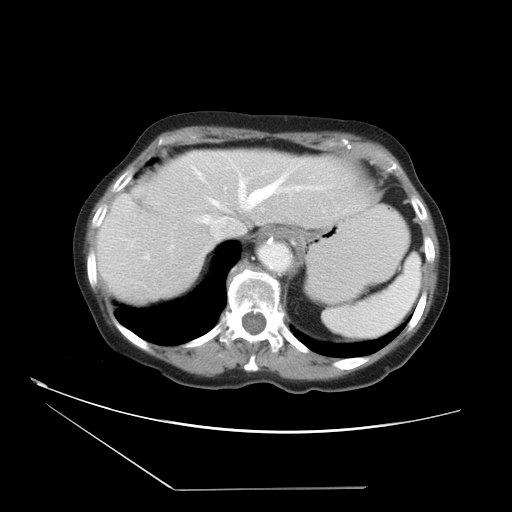
Contrast-enhanced abdominal CT, one axial slice; position 28 of 36 along the scan axis; 120 kVp; intravenous contrast given; soft-tissue window (W 400 / L 40 HU); 512 × 512 image matrix. Female patient, age 81 years. From the clinical record (not read from this slice): diagnosis: colorectal cancer liver metastases, imaged before liver resection; multiple liver metastases: no; largest metastasis: 1.6 cm.
Structures marked on this image (outlined manually by an expert reader):
- hepatic veins: bounding box [x1, y1, x2, y2] px = [193, 167, 312, 227]
- liver: [97, 149, 377, 305]
- planned liver remnant (the part of the liver to remain after resection): [97, 150, 377, 305]